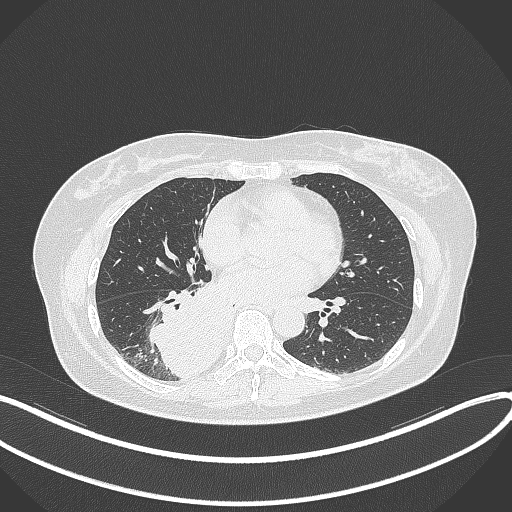
Chest CT, one axial slice. Position 161 of 331 along the scan axis. Reconstruction kernel B70f. 120 kVp. Lung window (W 1500 / L -600 HU). 1 mm slice thickness. 512 × 512 image matrix, field of view 400 × 400 mm. Patient: female, 54 years. From the clinical record (not read from this slice): clinical TNM (as recorded): T4 N0 M0.
Structures marked on this image (bounding box drawn by a radiologist):
- lung tumour (recorded histology: adenocarcinoma): bounding box <144,286,219,382> (left, top, right, bottom; pixels)